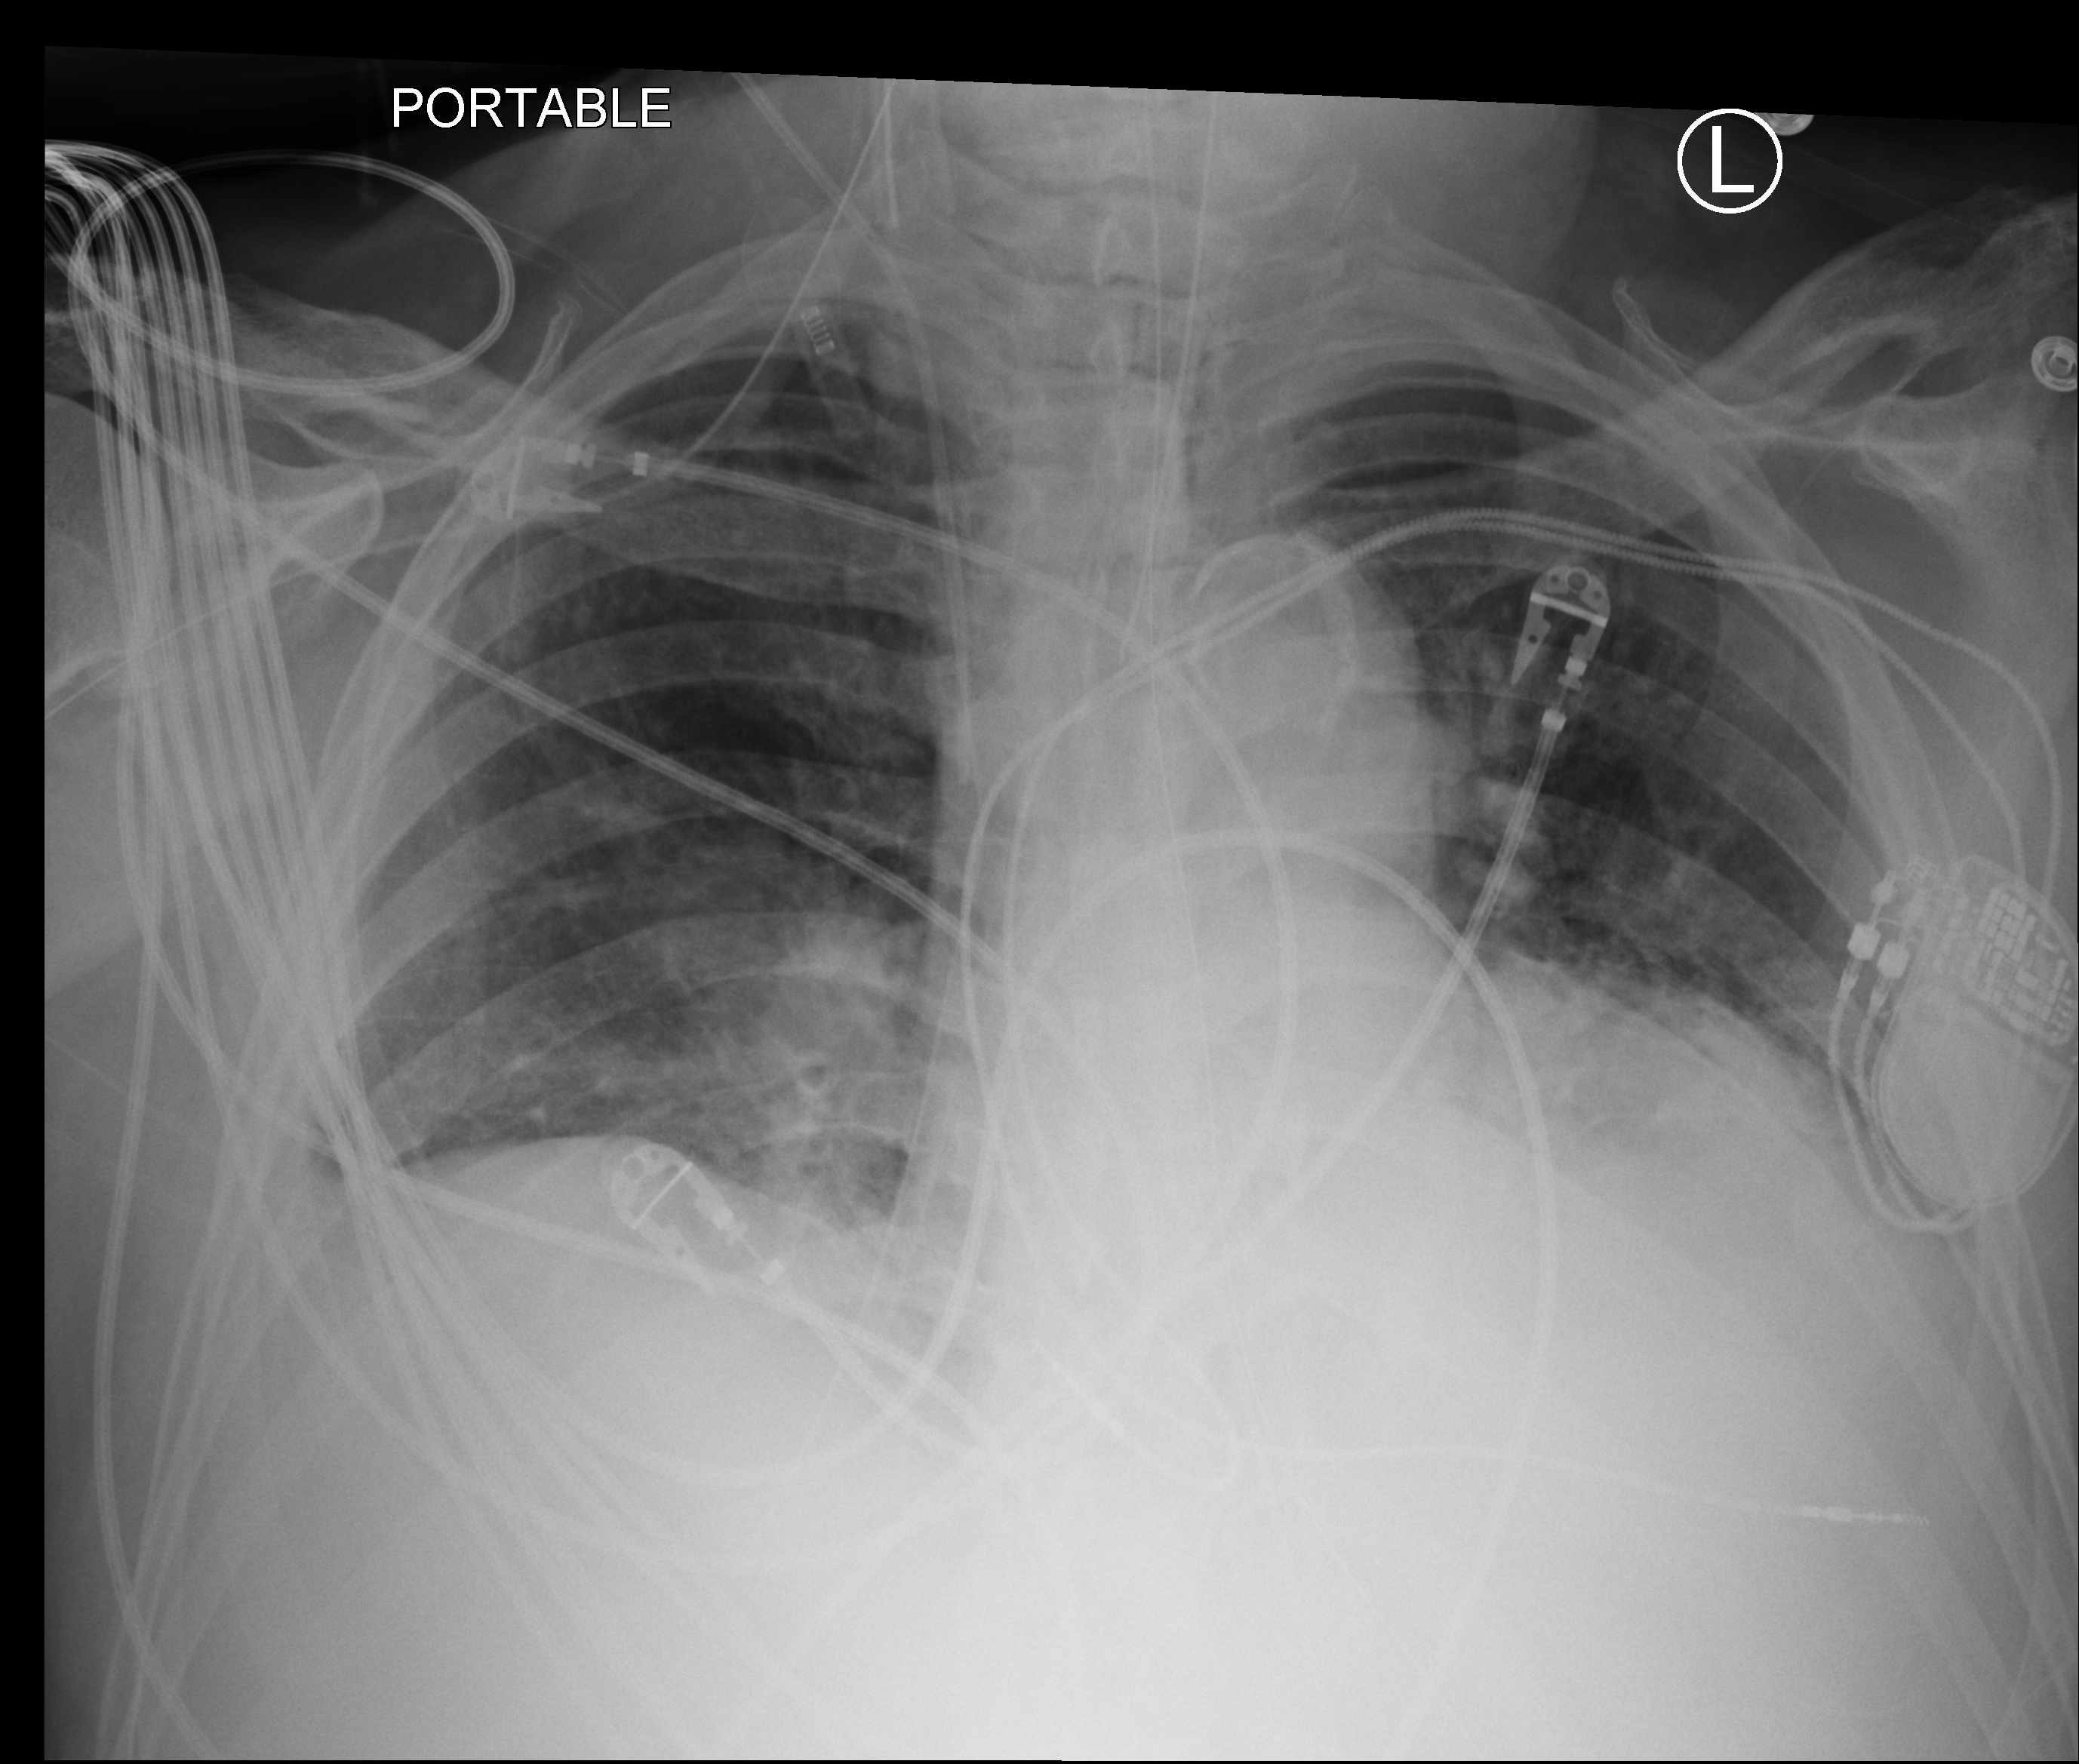
Chest X-ray (portable); anteroposterior (AP) projection. Patient hospitalised with COVID-19; male, aged 60–74 years.
Hospital-stay facts (about this admission, not read from this image; timing relative to this image not recorded): admitted to intensive care during this hospital stay: yes; length of hospital stay: 41 days.